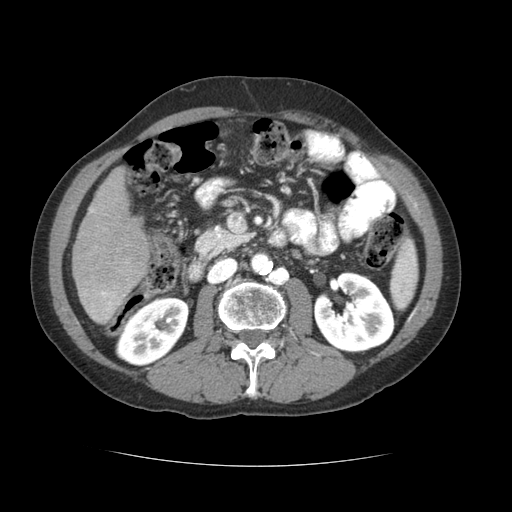
Contrast-enhanced abdominal CT (liver protocol), one axial slice; slice 20 of 69 in the series (ordered by position); reconstruction kernel STANDARD; soft-tissue window (W 400 / L 40 HU); 512 × 512 image matrix, field of view 360 × 360 mm. Case-level facts recorded for this patient, not image findings: diagnosis: hepatocellular carcinoma (patient treated with transarterial chemoembolisation; whether this scan precedes or follows treatment is not stated here); TNM stage (as recorded): Stage-II; Child-Pugh class: B; tumour differentiation: poorly differentiated; tumour nodularity: multinodular.
Outlined on this slice (semi-automatically segmented with operator editing):
- liver parenchyma outside the tumour (the mass and vessels are separate outlines, so this box may not span the whole liver): bounding box (x1, y1, x2, y2) in pixels: (72, 168, 148, 324)
- liver vessels: (84, 209, 125, 318)